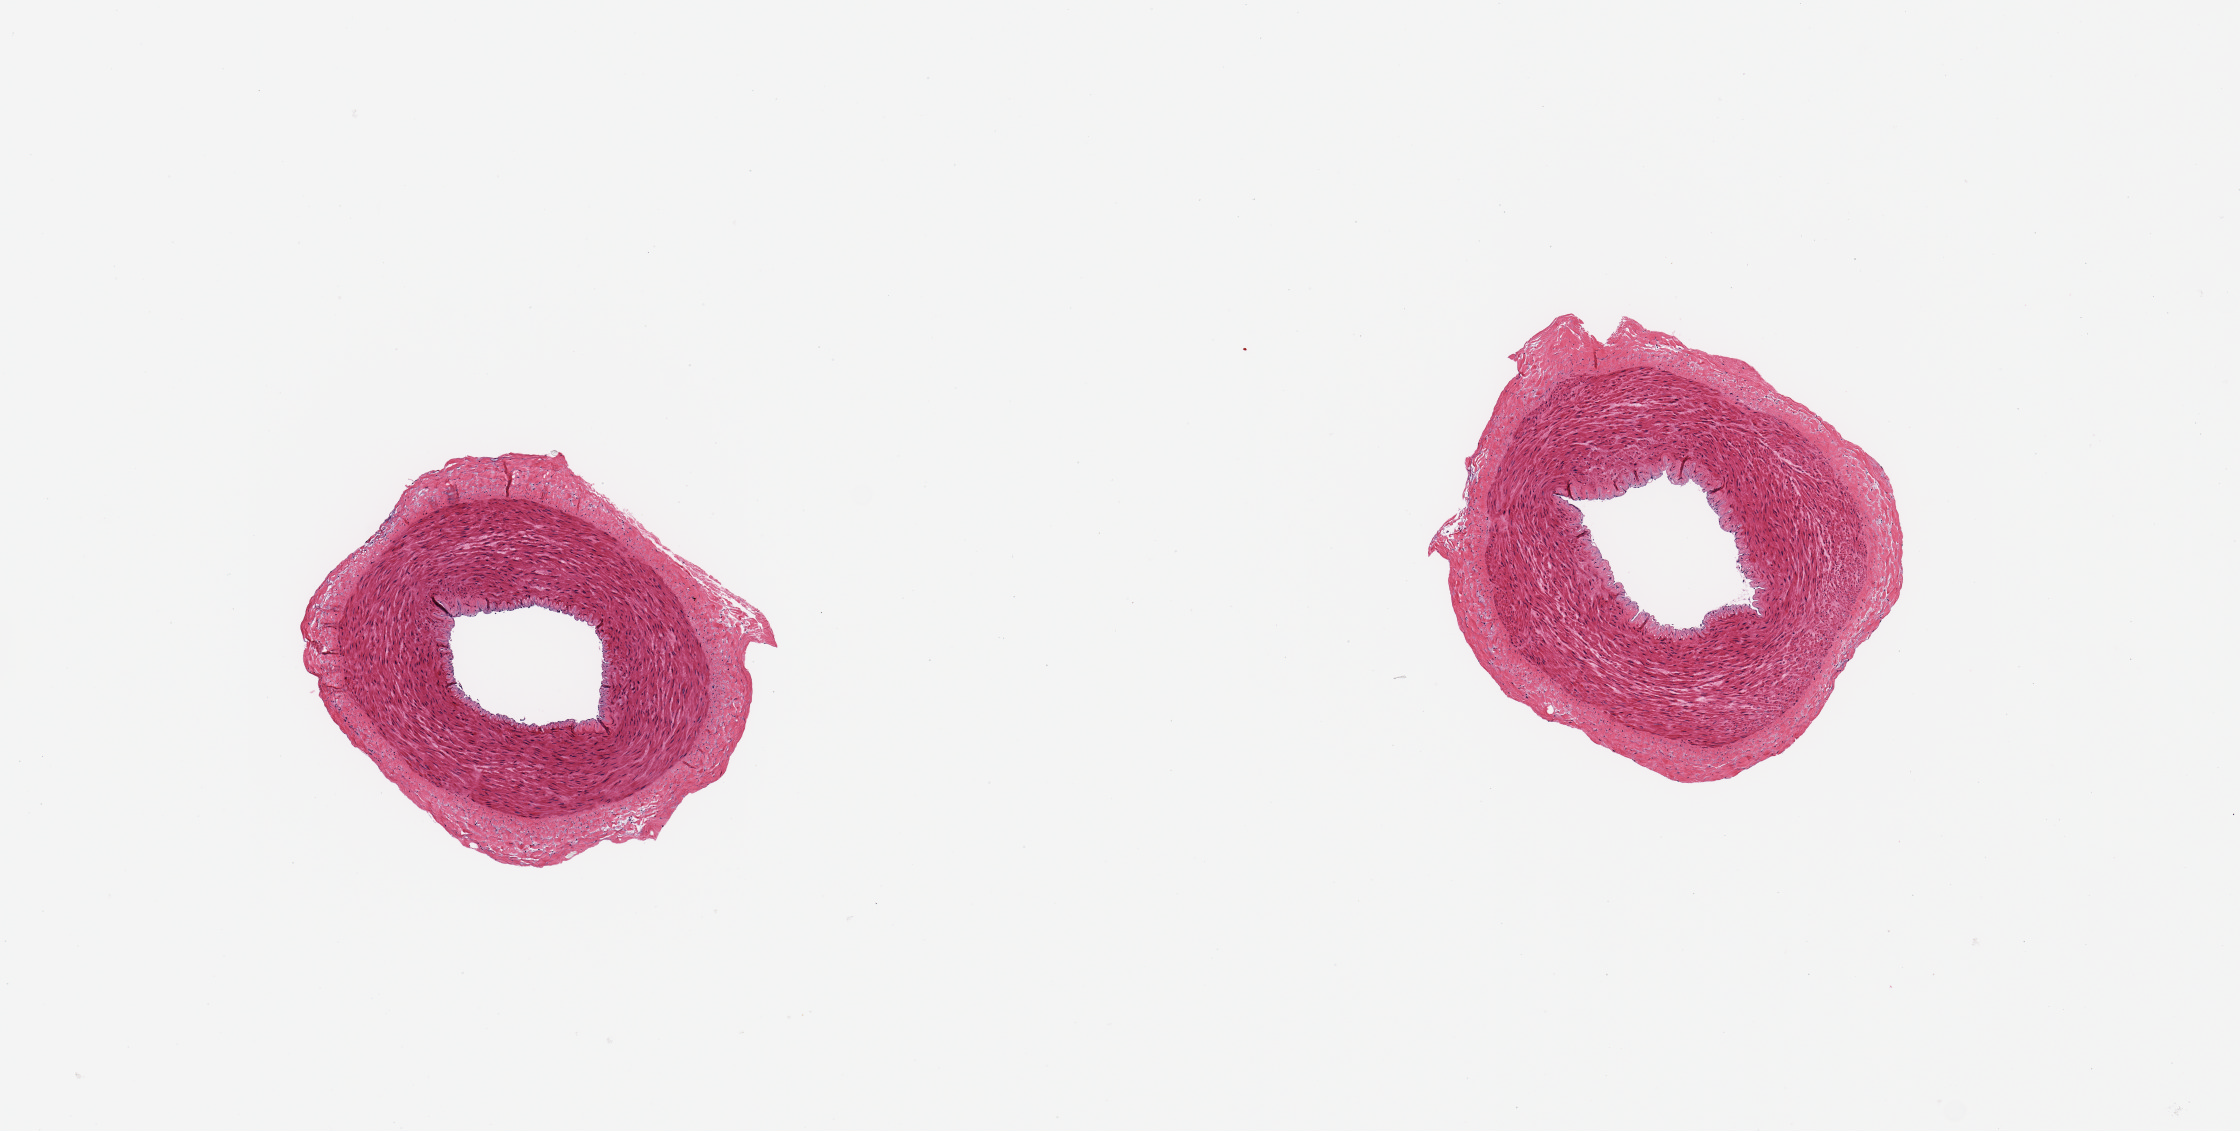
H&E whole-slide image — low-resolution overview of the scanned area, about 8.9 x 4.5 mm. PAXgene-fixed, paraffin-embedded tissue. Target tissue: tibial artery. Donor tissue sample. Donor: male.
Review note (as recorded): 2 pieces; ~0.25mm rim of adventitia.